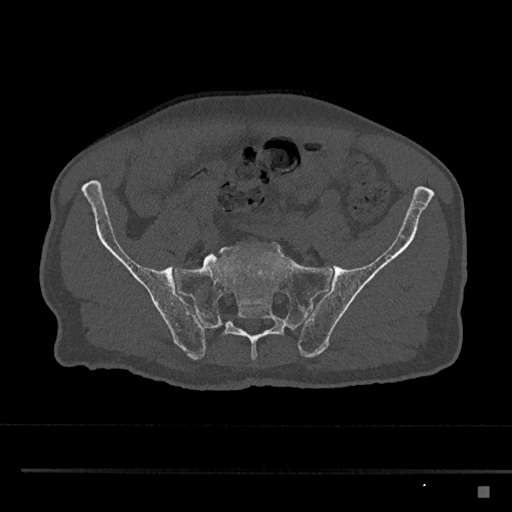
CT including the spine, one axial slice; position 513 of 797 along the scan axis; reconstruction kernel Br40s/3; 120 kVp; bone window (W 1800 / L 400 HU); 0.5 mm slice thickness; 512 × 512 image matrix, field of view 391 × 391 mm. Patient: male, 59 years. Case-level facts recorded for this patient, not image findings: primary cancer: prostate.
Annotated regions visible in this slice (semi-automatically segmented with operator editing):
- L5 vertebra: box from (x=206, y=255) to (x=210, y=258) px